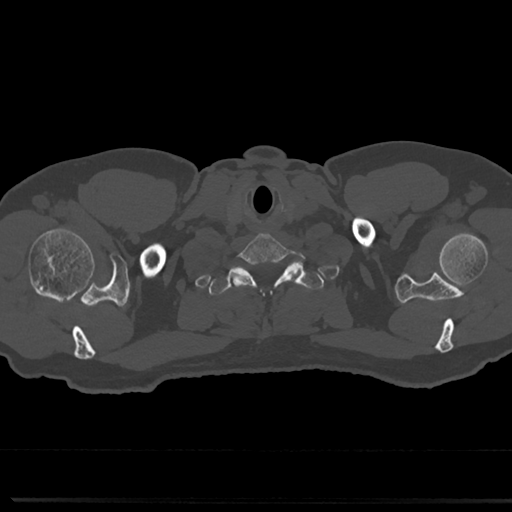
CT including the spine, one axial slice. Slice 691 of 817 in the series (ordered by position). Reconstruction kernel Br40s/3. 120 kVp. Bone window (W 1800 / L 400 HU). 512 × 512 image matrix, field of view 355 × 355 mm. Patient: male, 61 years. From the clinical record (not read from this slice): primary cancer: prostate.
Outlined on this slice (semi-automatically segmented with operator editing):
- T1 vertebra: bounding box (x1, y1, x2, y2) in pixels: (210, 262, 318, 342)